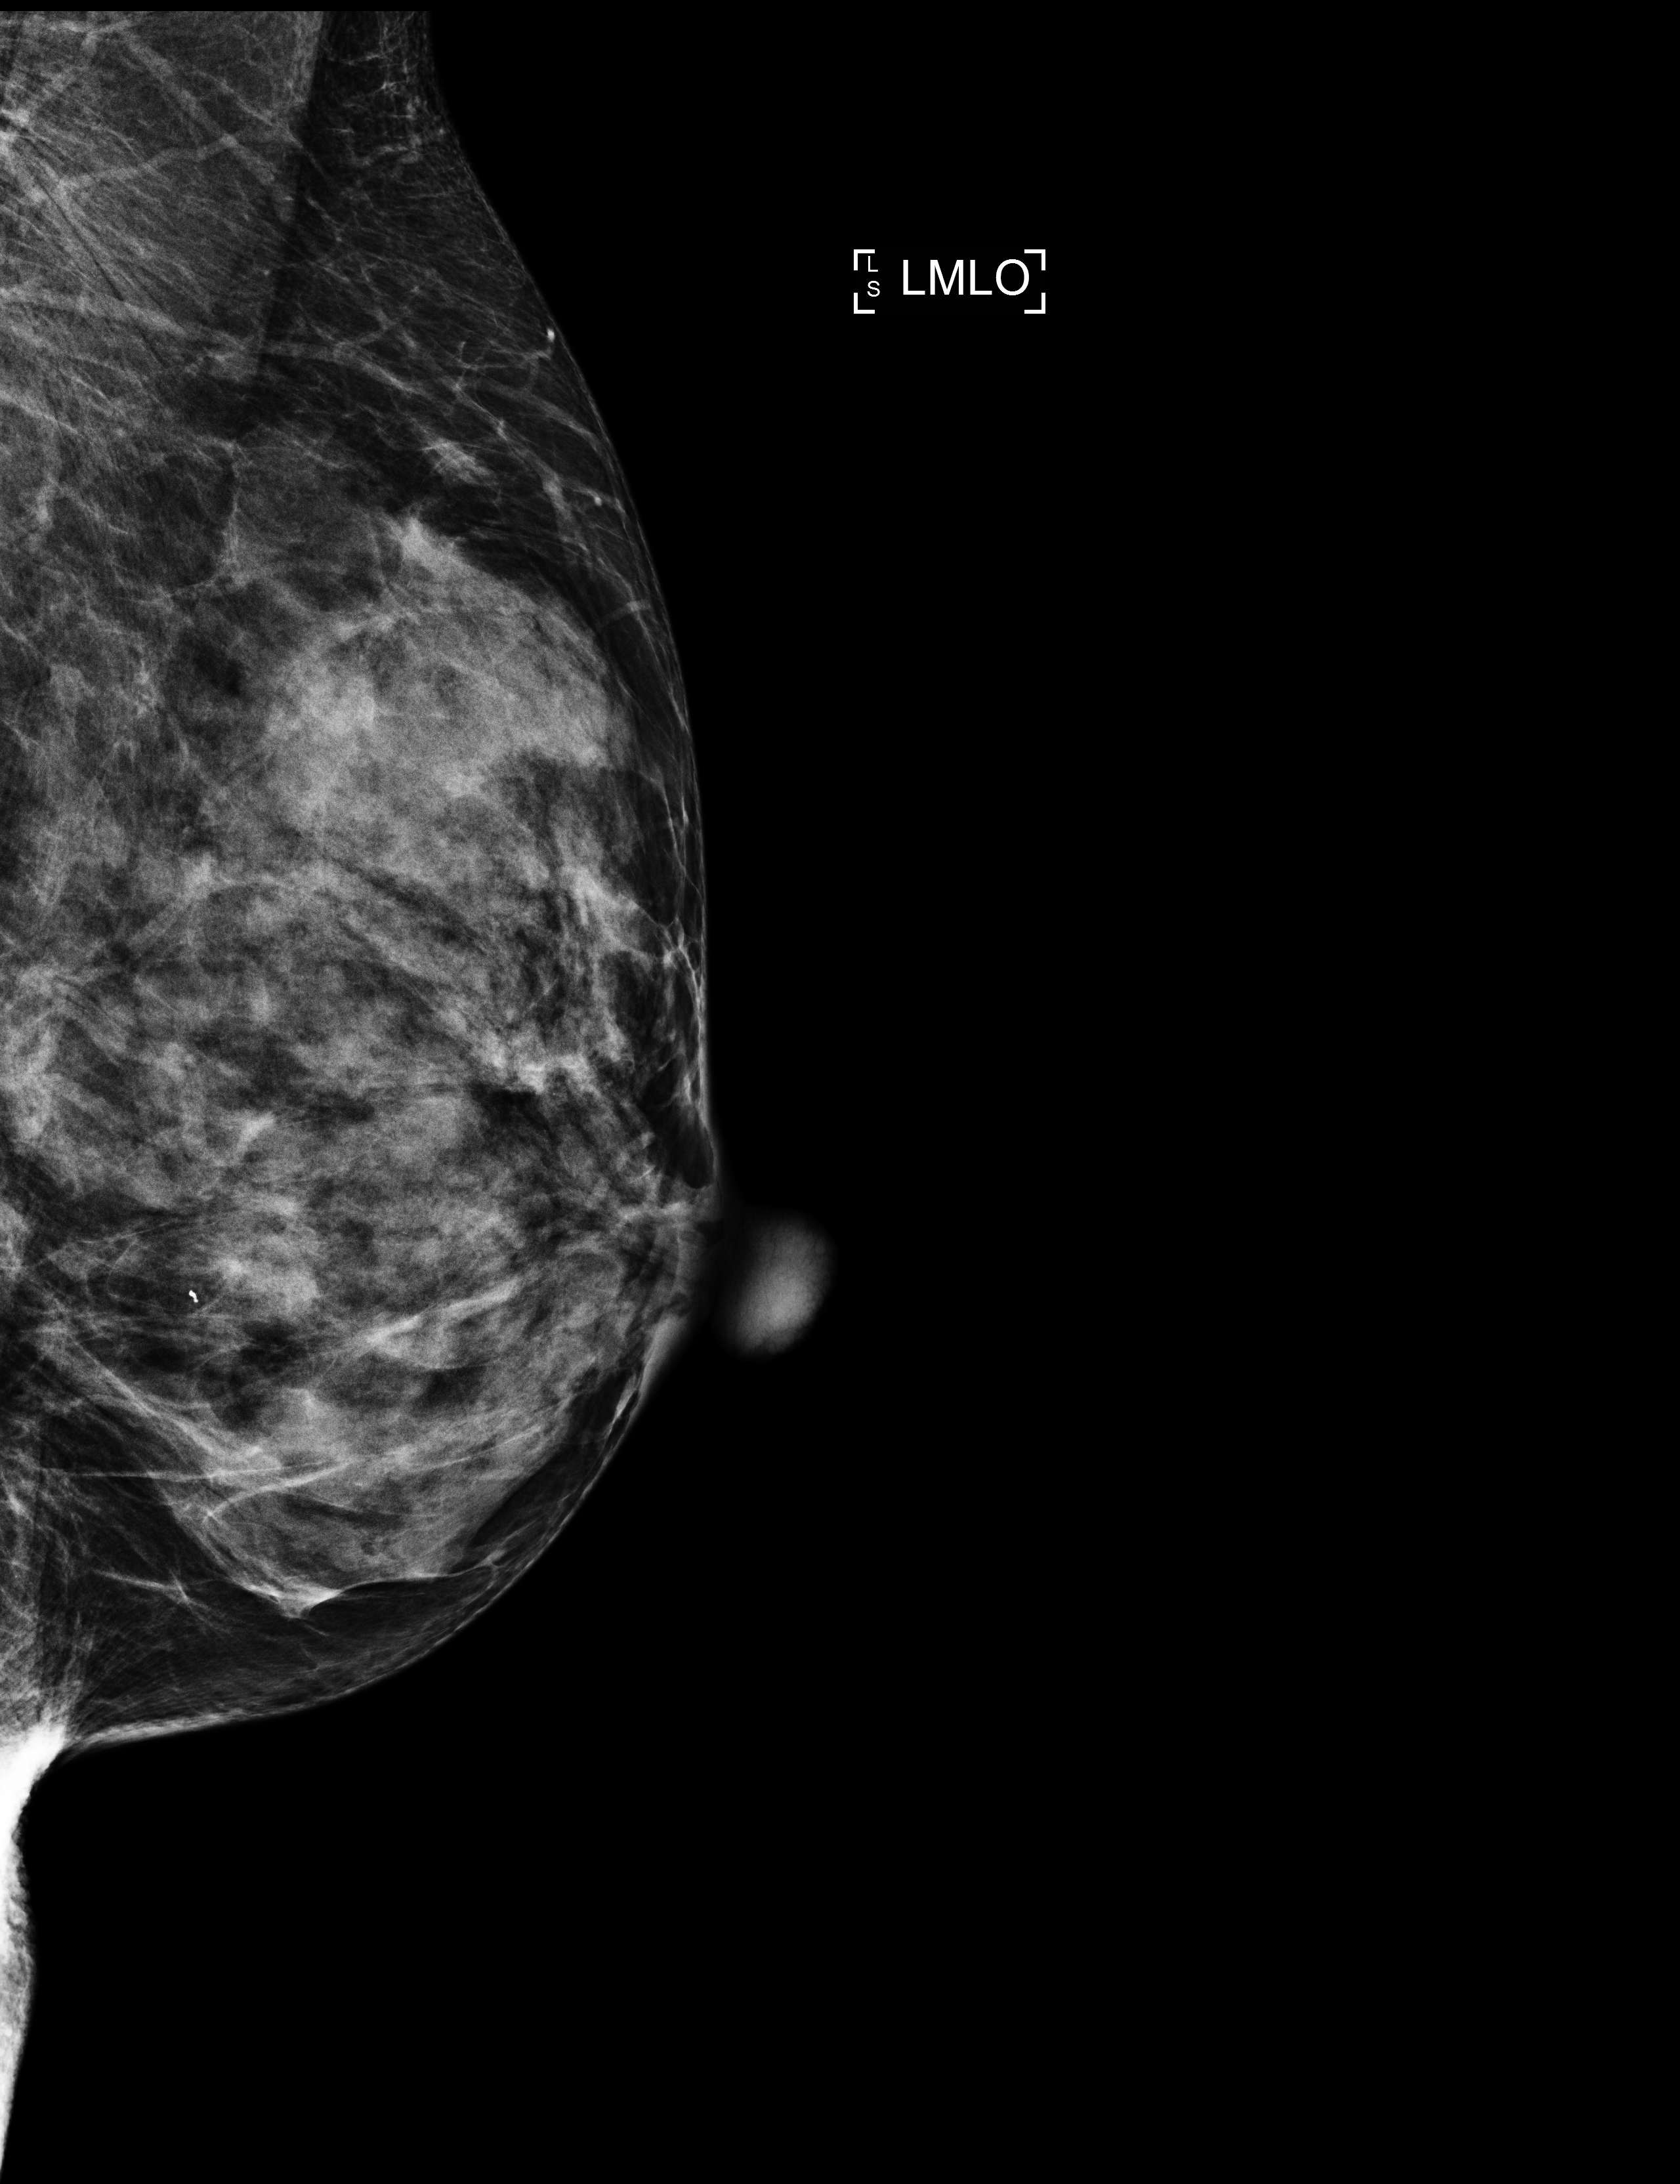
Screening examination, system: Selenia Dimensions. Female patient, age 68 years.
Image type: full-field digital mammogram. Breast: left. Projection: medio-lateral oblique projection.